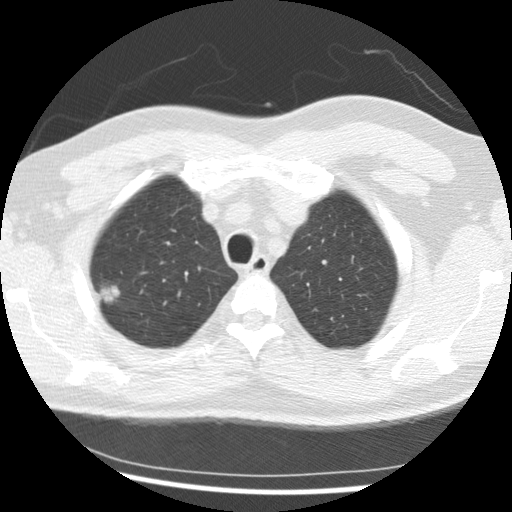
Axial slice from a low-dose chest CT screening exam; first (baseline) screen; lung window (W 1500 / L -600 HU); standard (soft-tissue) reconstruction kernel (STANDARD); slice 48 of 265 in the series; 512 × 512 image matrix, field of view 340 × 340 mm. Male participant, aged 56 years at enrolment. Current smoker at enrolment.
Expert reader's lesion annotation, bounding box (x1, y1, x2, y2) in pixels: (85, 274, 132, 315). Screening reader's record for this exam (one nodule recorded; not confirmed to be the boxed lesion): non-calcified nodule or mass ≥4 mm, right upper lobe, 19 × 15 mm, spiculated (stellate) margins, soft tissue attenuation. Later outcome: lung cancer diagnosed 291 days after this screen — non-small cell carcinoma, right upper lobe, poorly differentiated (G3), stage IIIB (AJCC 6th edition), 20 mm at pathology.